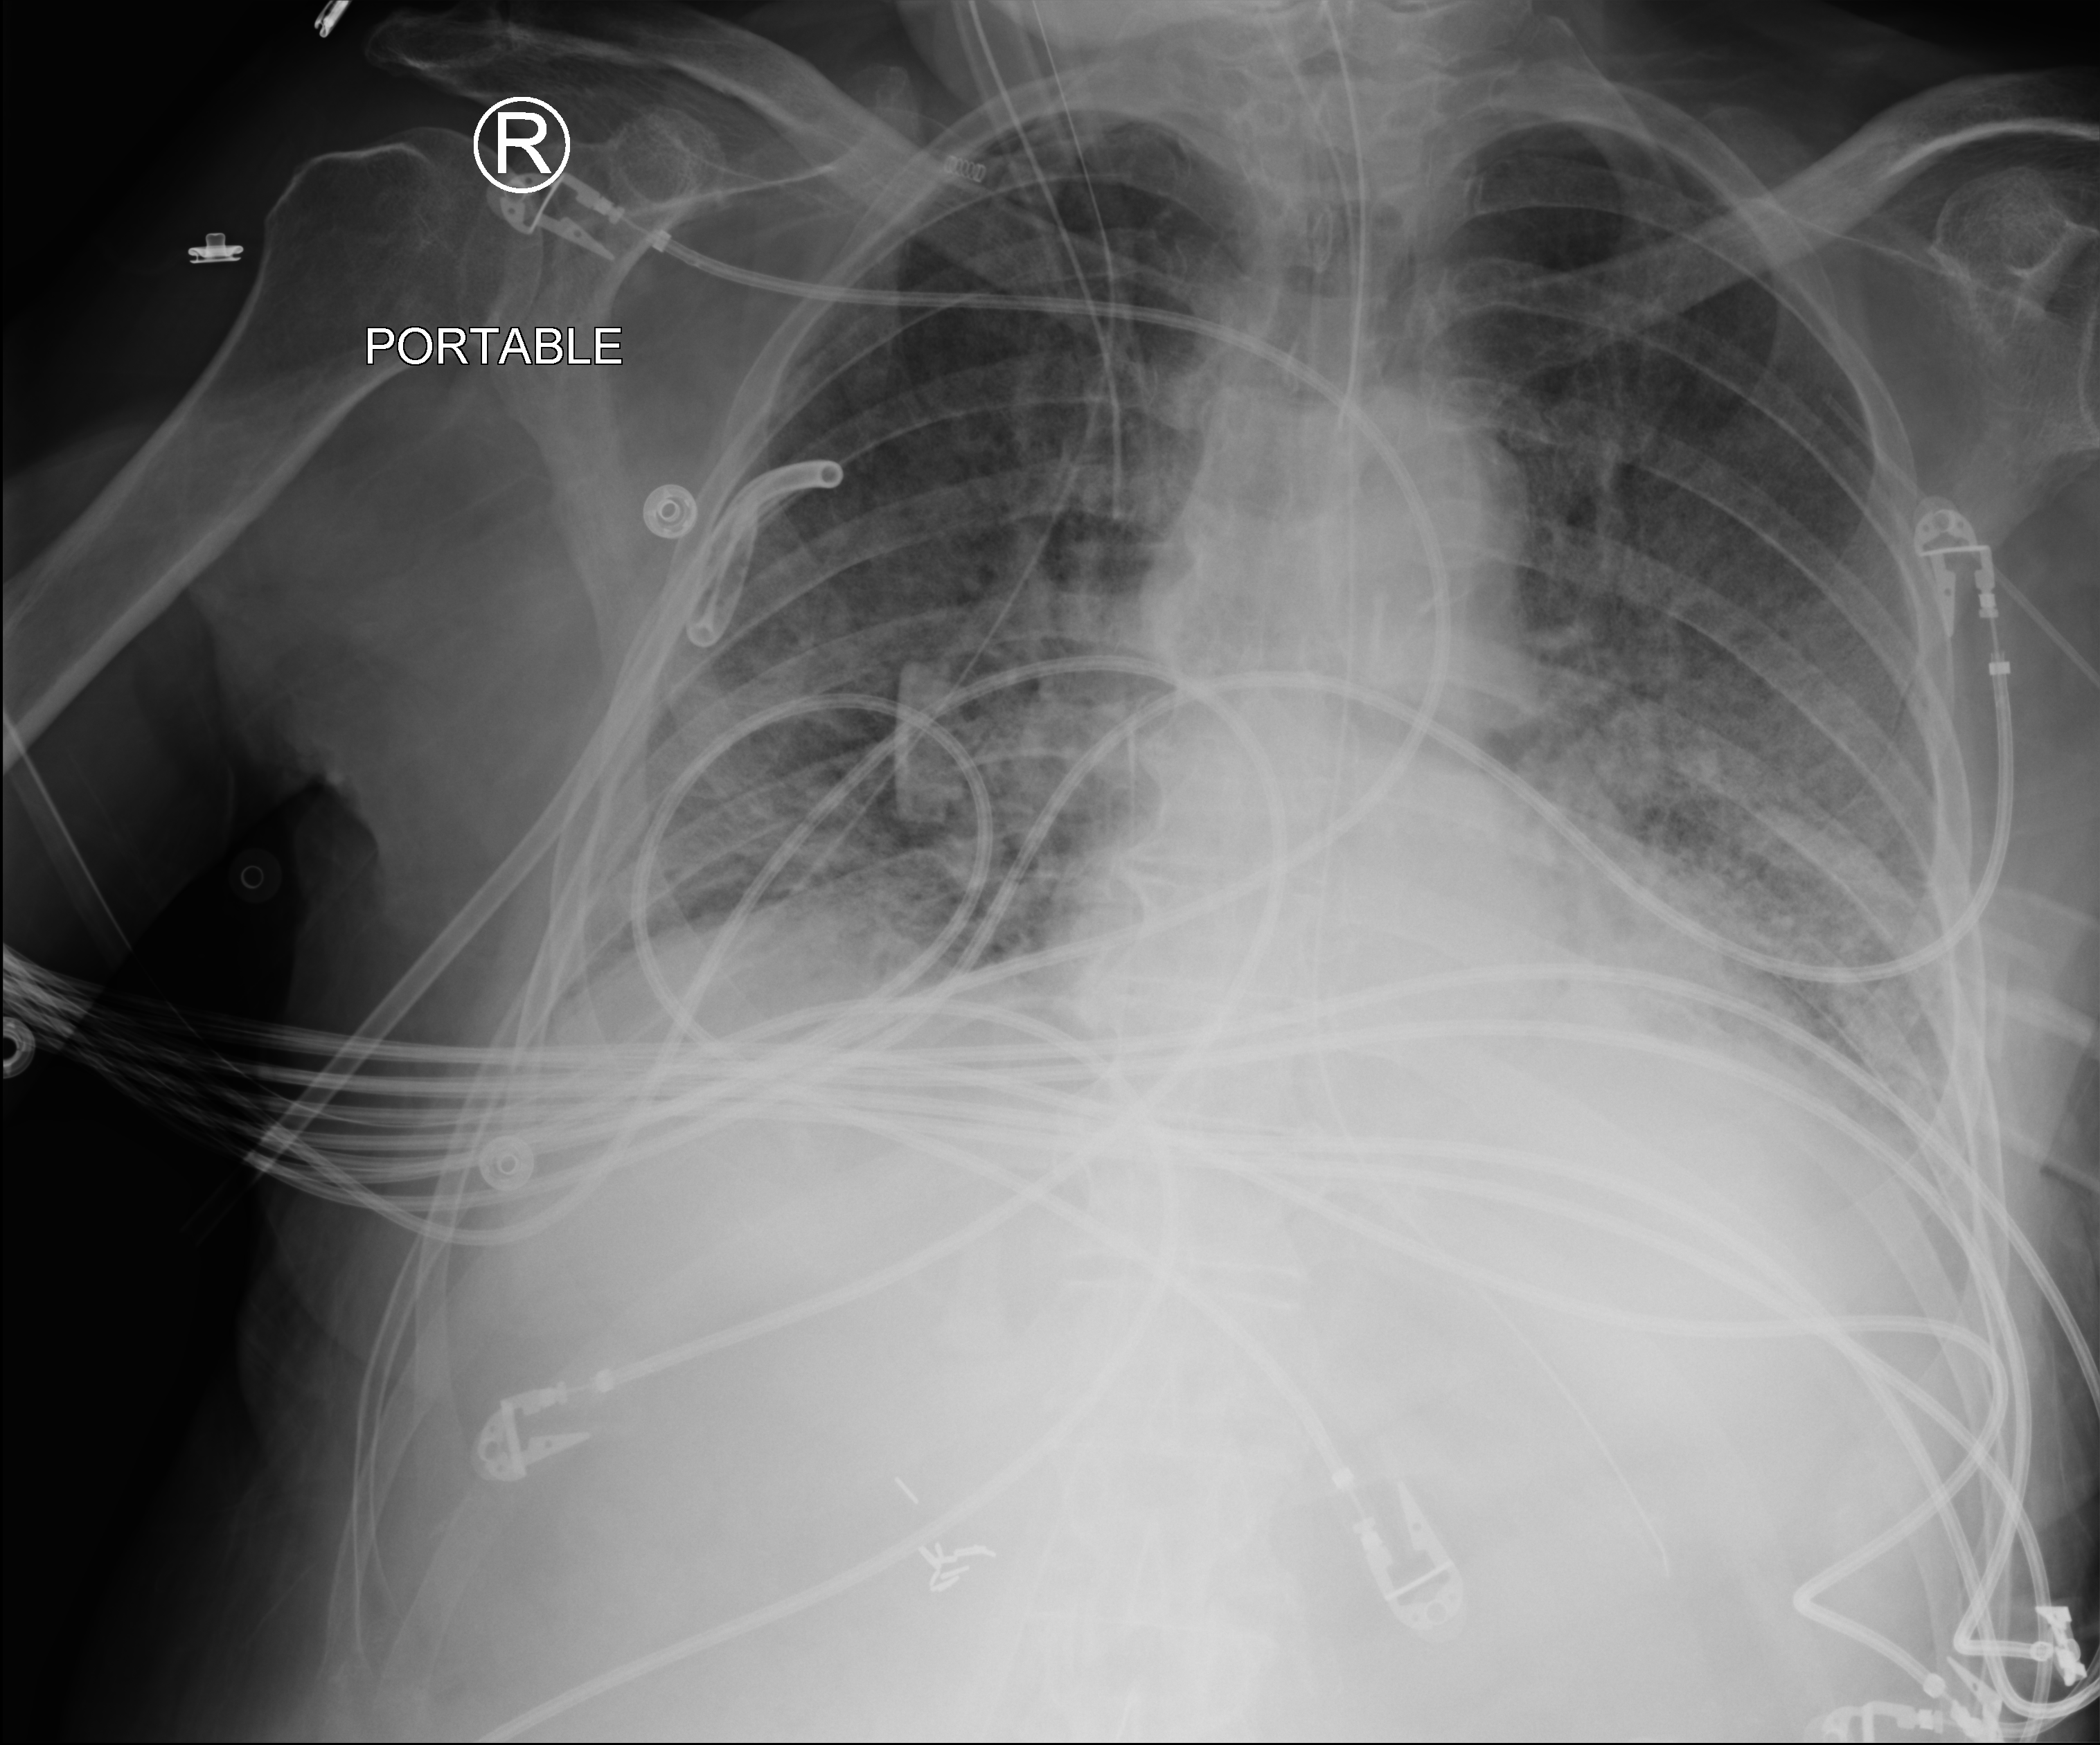
Chest X-ray (portable), anteroposterior (AP) projection. Male patient hospitalised with COVID-19, age 75–90 years.
From the hospital-stay record, not from the radiograph (when in the stay this image was taken is not recorded): other chronic lung disease (admission record): no; length of hospital stay: 23 days.